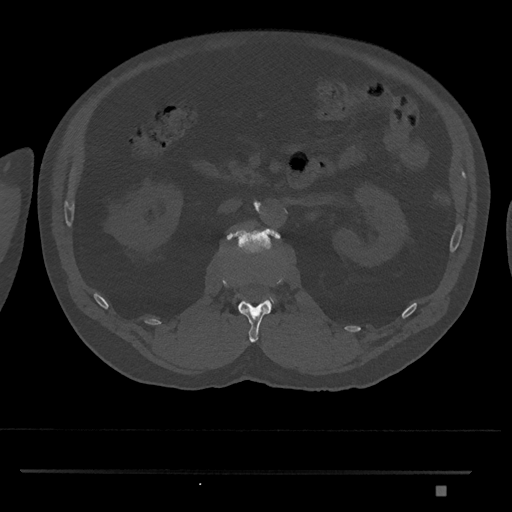
CT including the spine, one axial slice; reconstruction kernel Br40s/3; 120 kVp; bone window (W 1800 / L 400 HU); 0.5 mm slice thickness; 512 × 512 image matrix, field of view 429 × 429 mm. Male patient, age 65 years. Case-level facts recorded for this patient, not image findings: primary cancer: prostate.
Structures marked on this image (semi-automatic segmentation, software-assisted and operator-edited):
- L1 vertebra: box from (x=238, y=275) to (x=284, y=343) px
- L2 vertebra: (x=226, y=228)–(x=281, y=303)